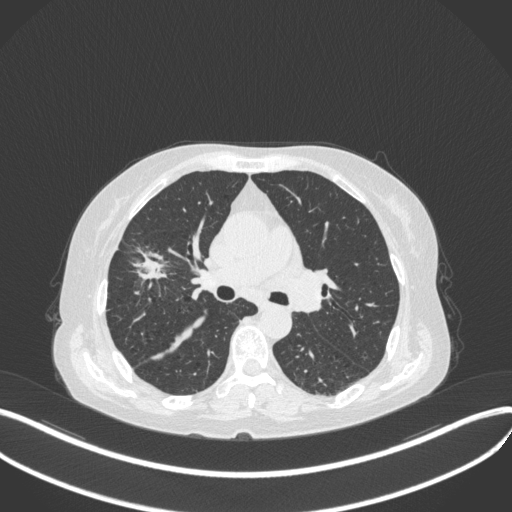
Chest CT, one axial slice; position 241 of 429 along the scan axis; 120 kVp; lung window (W 1500 / L -600 HU); 512 × 512 image matrix, field of view 400 × 400 mm. Female patient, age 69 years. Case-level facts recorded for this patient, not image findings: clinical TNM (as recorded): T1b N3 M0.
Annotated regions visible in this slice (rectangle marked by the reading radiologist):
- lung tumour (recorded histology: small cell carcinoma): bounding box (x1, y1, x2, y2) in pixels: (124, 241, 178, 289)